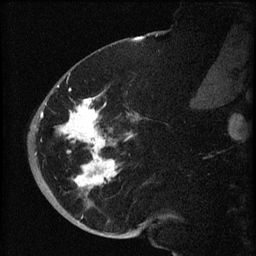
Breast MRI (dynamic contrast-enhanced), one sagittal slice. Position 24 of 60 along the scan axis. Dynamic contrast-enhanced series, image 2 of 3 at this slice position (ordered by acquisition). 1.5 T. TE 4.2 ms, TR 8.2 ms. 2 mm slice thickness. 256 × 256 image matrix. Patient: female, 71 years.
Annotated regions visible in this slice (semi-automatically segmented with operator editing):
- analysis volume of interest (the breast-tissue region the enhancement analysis was run in; not a lesion): bounding box (x1, y1, x2, y2) in pixels: (40, 72, 148, 196)
- tumour enhancement mask (voxels above the 70 % enhancement threshold inside the analysis volume of interest): (40, 85, 132, 190)